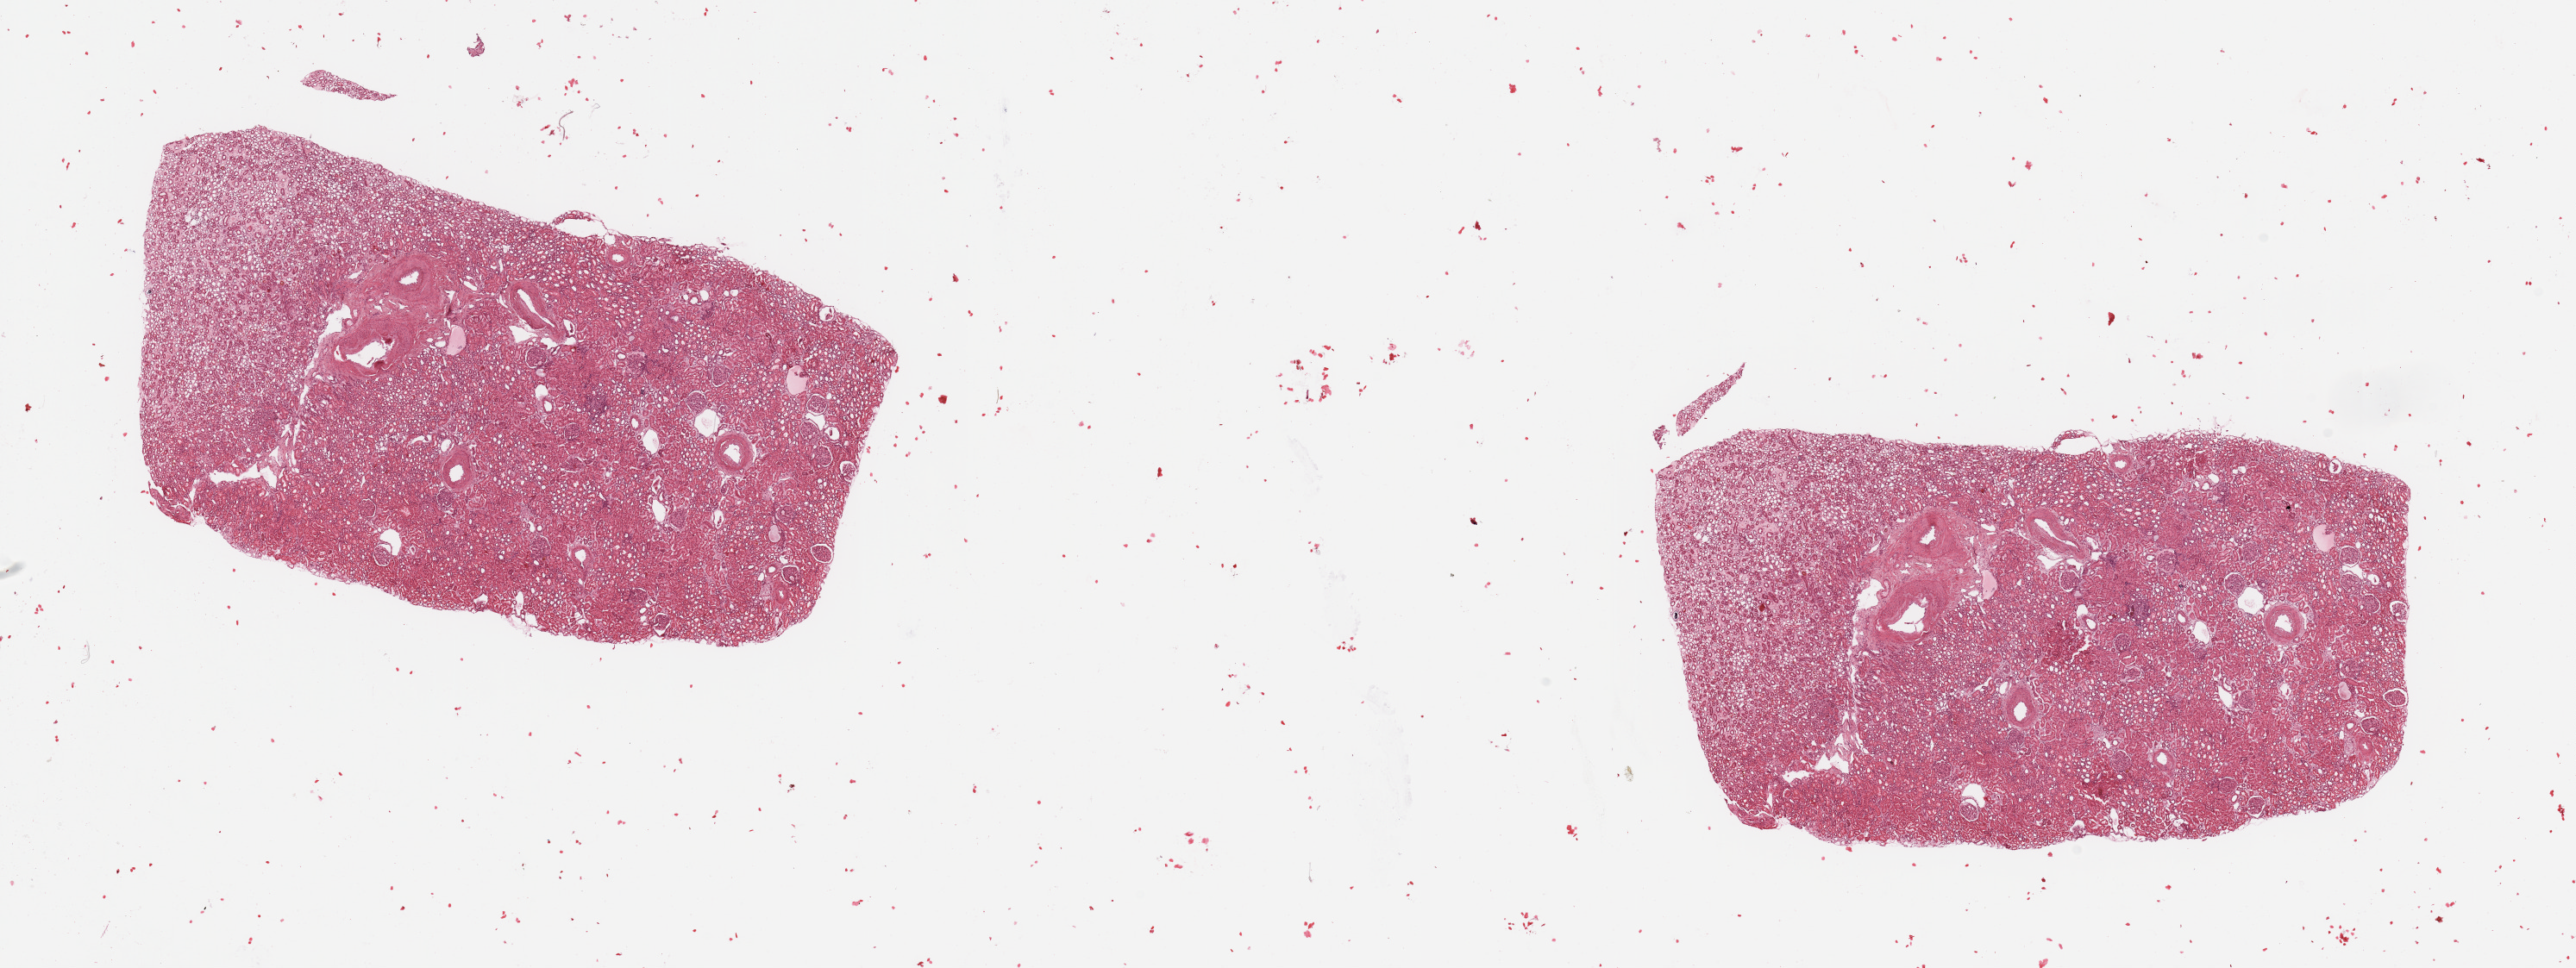
Whole-slide histology image, Hematoxylin and eosin (H&E) stained, low-resolution overview of the scanned area, about 23.6 x 8.9 mm (slide scanned at 20x); normal (non-tumour) tissue sample, sampled site: kidney. Male, 65 y/o.
This section: normal (non-tumour) tissue from the same patient. Patient diagnosis: Renal cell carcinoma, NOS.